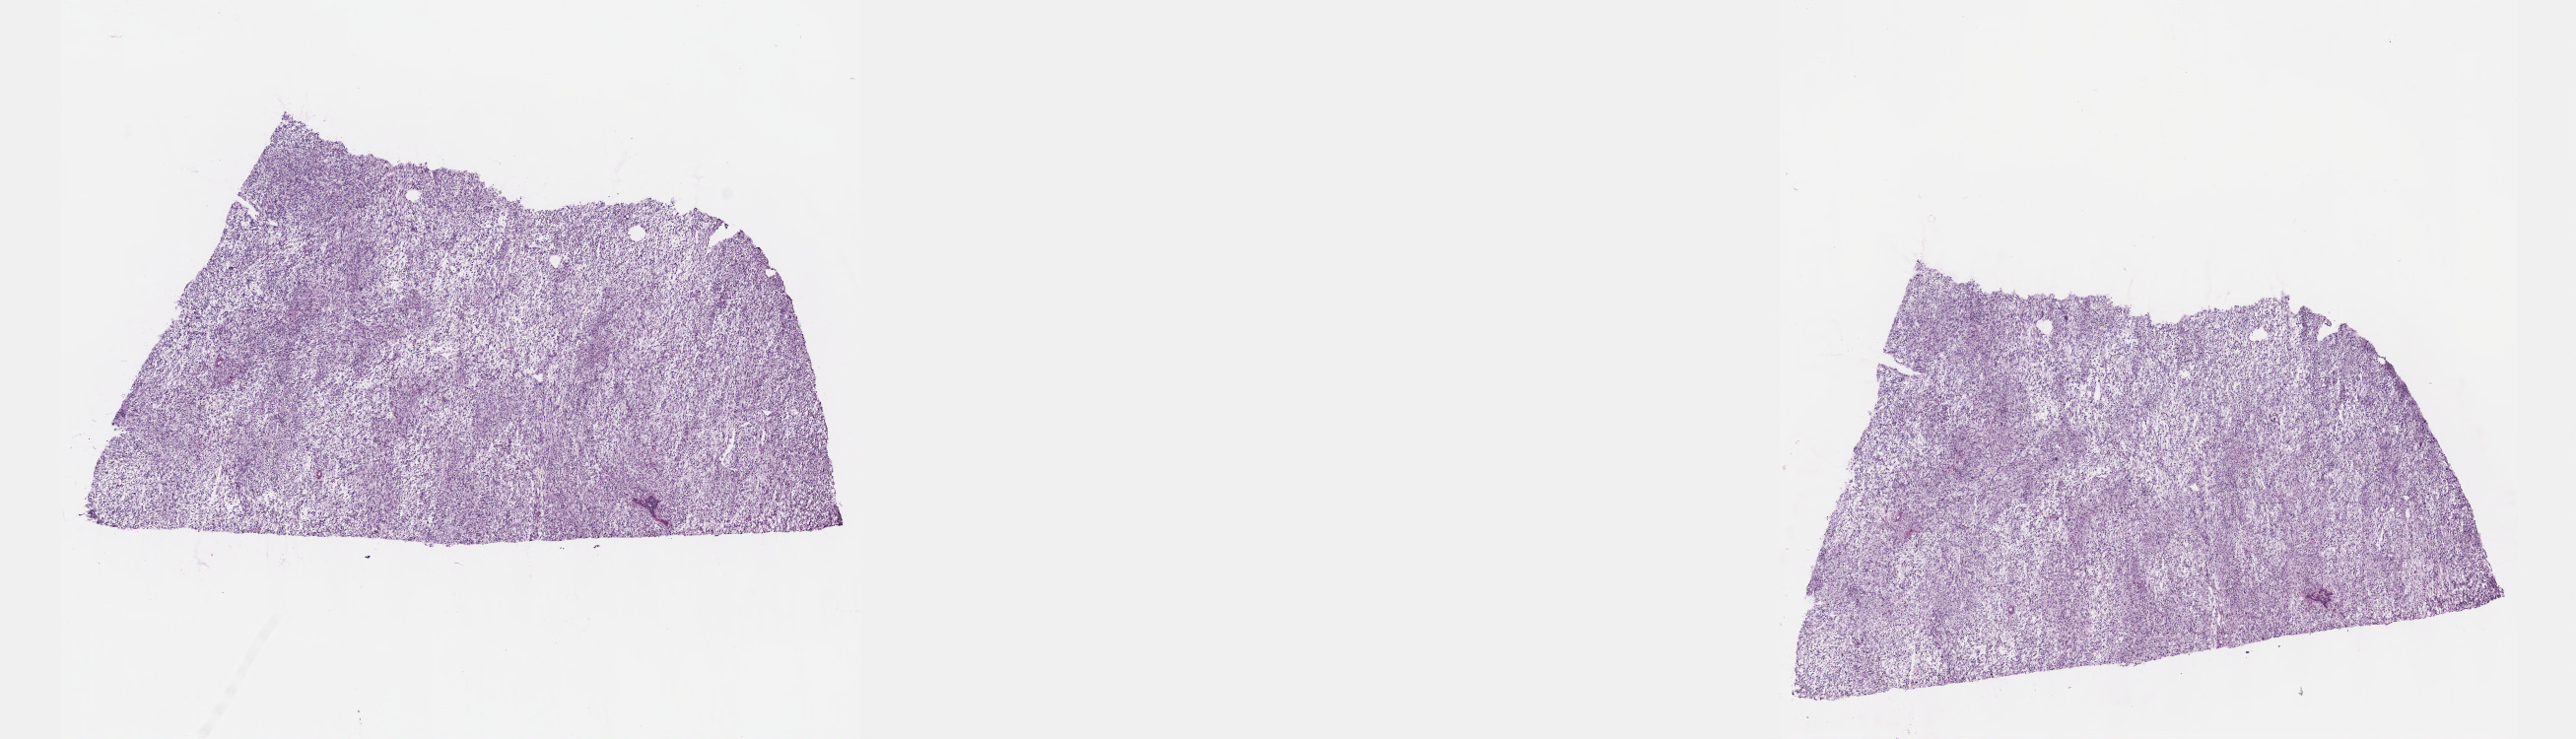
Digitized H&E tissue section (whole slide) — low-resolution overview of the scanned area, about 21.1 x 6.1 mm (acquisition: 40x scan). Frozen section. Primary tumour sample from the connective, subcutaneous and other soft tissues. Patient: female, age at initial diagnosis 53 years. Pathologist review of this section (percent, as recorded): tumour cells 100%, tumour nuclei 80%, normal cells 0%, stromal cells 0%, necrosis 0%. Infiltration values recorded for this section: lymphocyte infiltration 2%, monocyte infiltration 0%, neutrophil infiltration 0%.
Pathologic diagnosis: Leiomyosarcoma, NOS (connective, subcutaneous and other soft tissues of thorax).